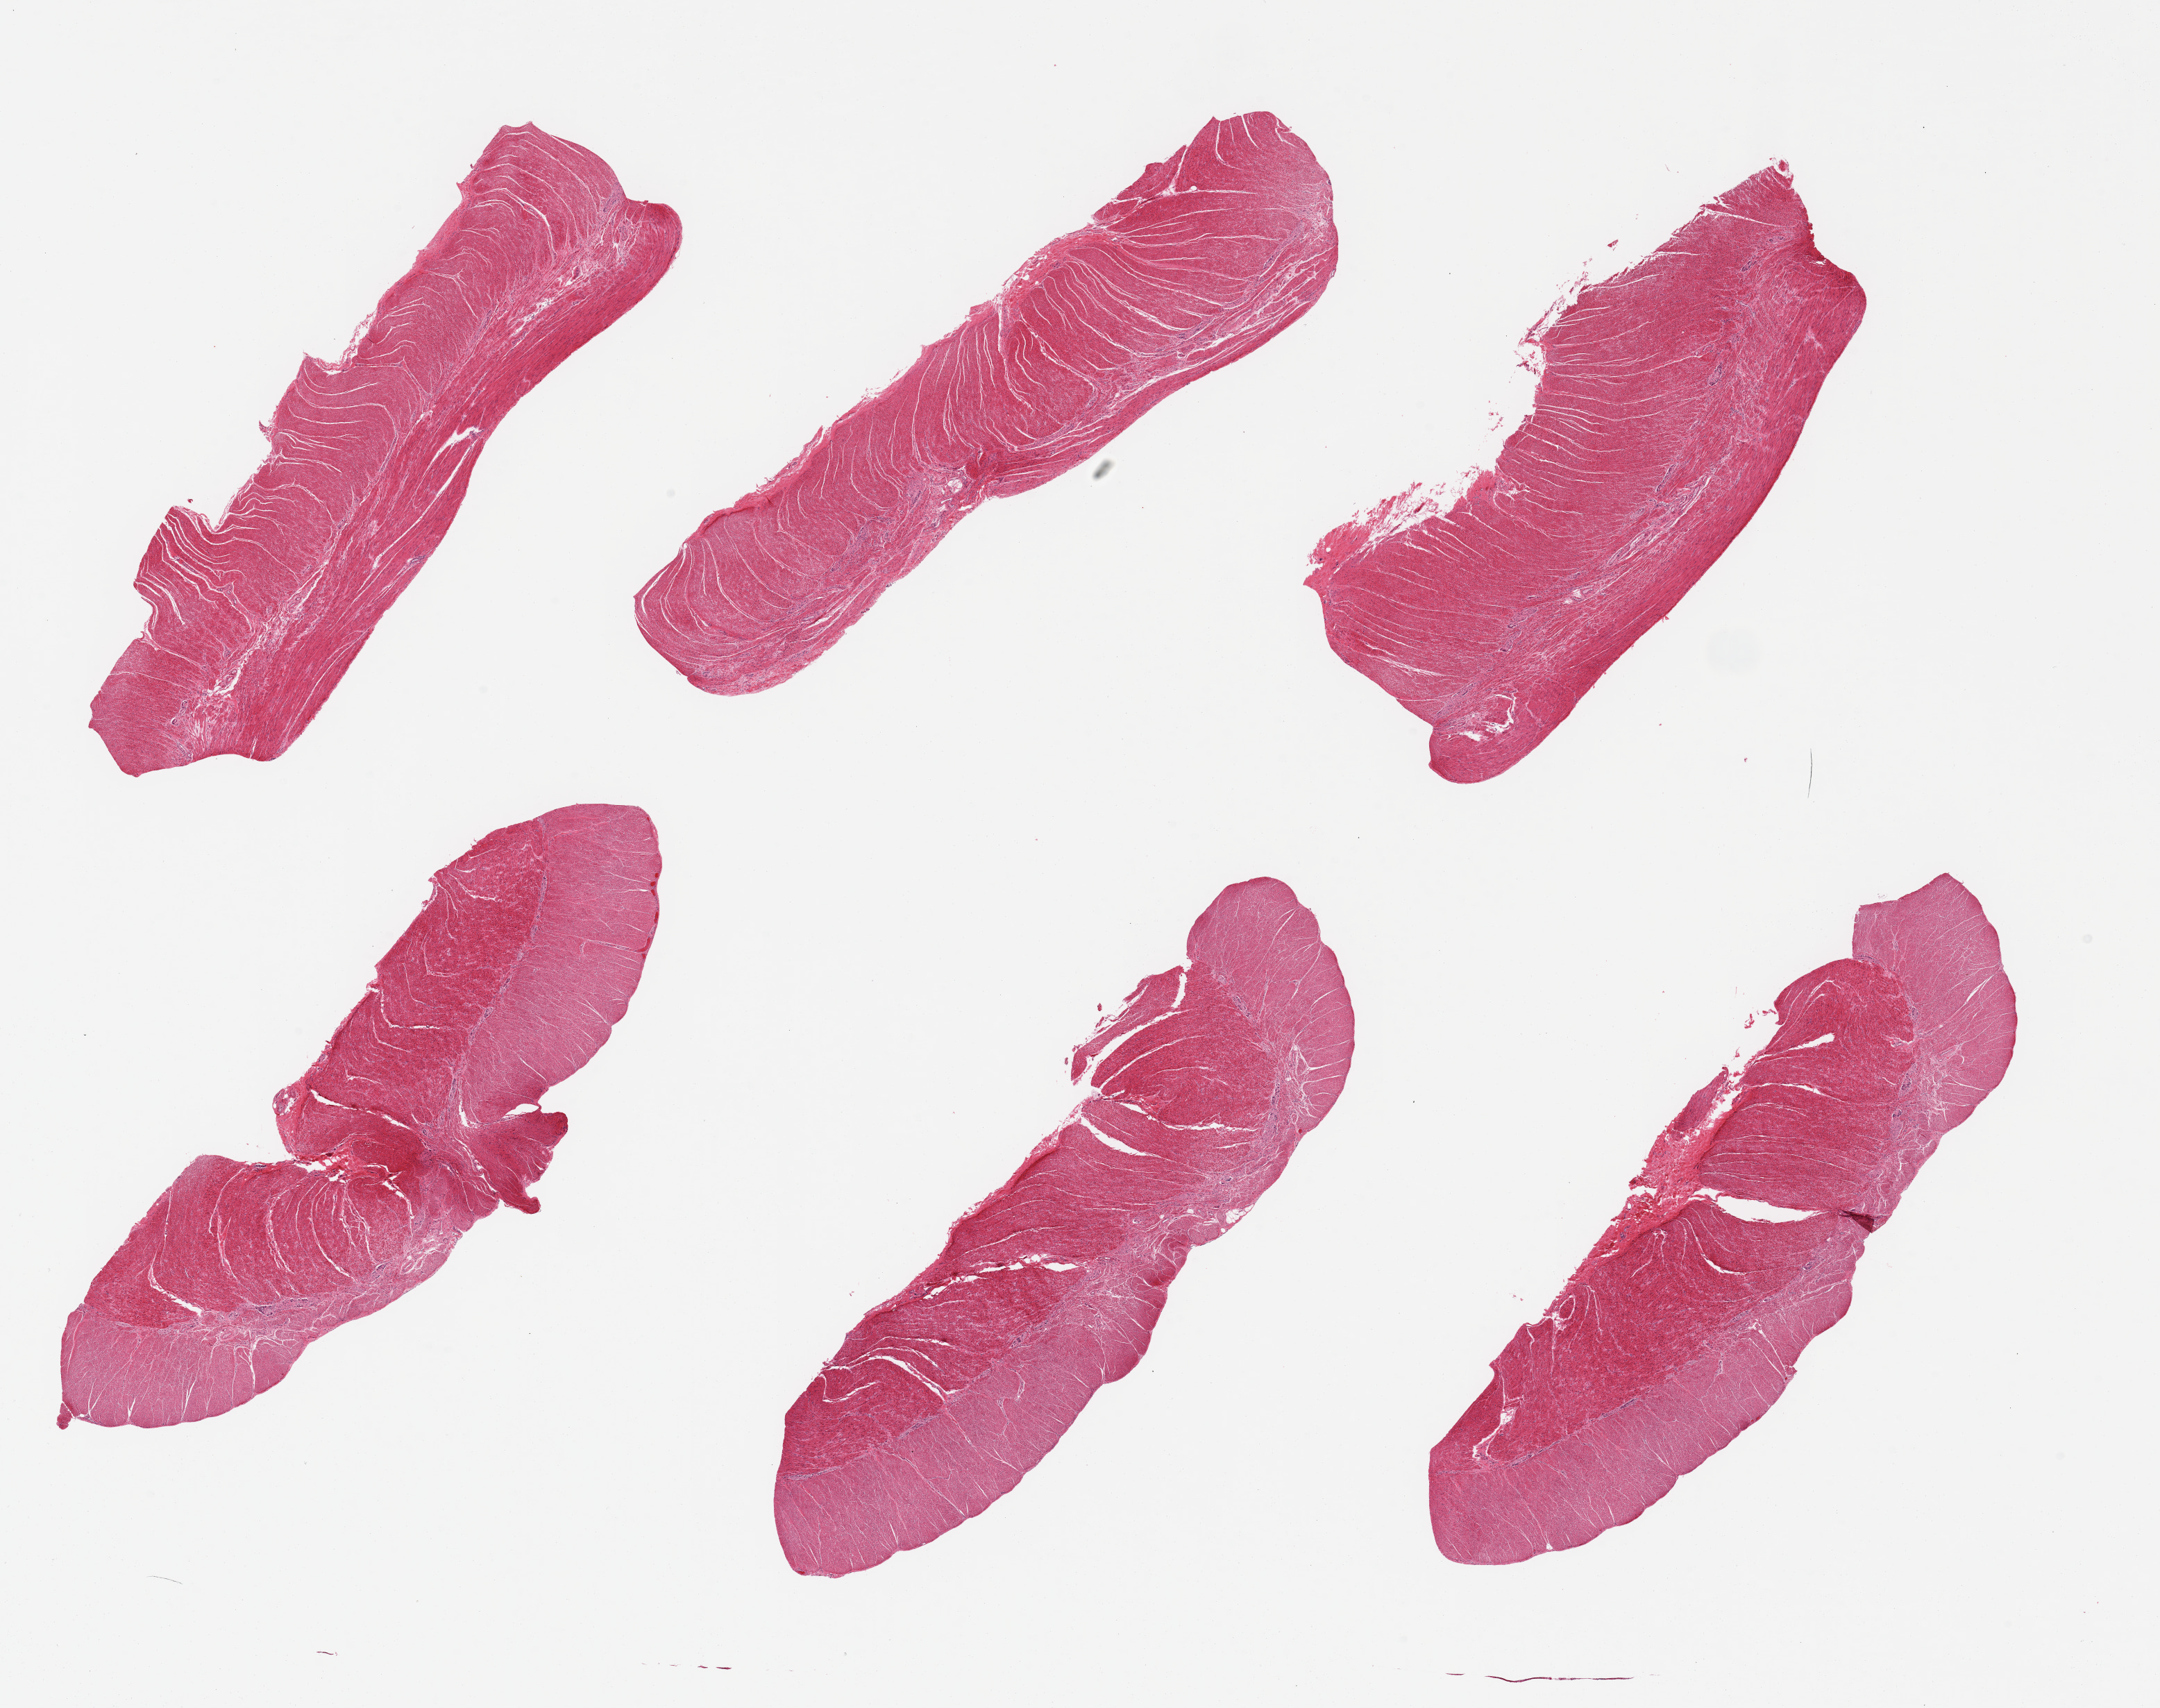
Digitized hematoxylin and eosin (H&E)-stained section — low-resolution overview of the scanned area, about 24.6 x 19.5 mm. PAXgene-fixed, paraffin-embedded tissue. Sampled site (target tissue): sigmoid colon. Donor tissue sample. Male donor.
- reviewer comment on this tissue sample: 5 pieces, well trimmed target muscularis